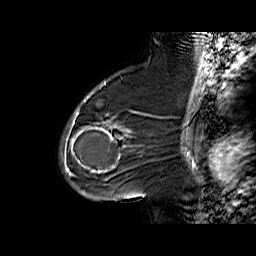
Breast MRI (dynamic contrast-enhanced), one sagittal slice; position 41 of 60 along the scan axis; dynamic contrast-enhanced series, time point 2 of 6 at this slice position (early post-contrast); 1.5 T; TE 6.3 ms, TR 32.4 ms; 256 × 256 image matrix, field of view 200 × 200 mm. Female patient. From the clinical record (not read from this slice): setting: breast cancer imaged before/during neoadjuvant chemotherapy; receptor status: triple-negative.
Outlined on this slice (semi-automatically segmented with operator editing):
- analysis volume of interest (the breast-tissue region the enhancement analysis was run in; not a lesion): bounding box [x1, y1, x2, y2] px = [65, 88, 140, 187]
- tumour enhancement mask (voxels above the 100 % enhancement threshold inside the analysis volume of interest): [65, 97, 130, 173]